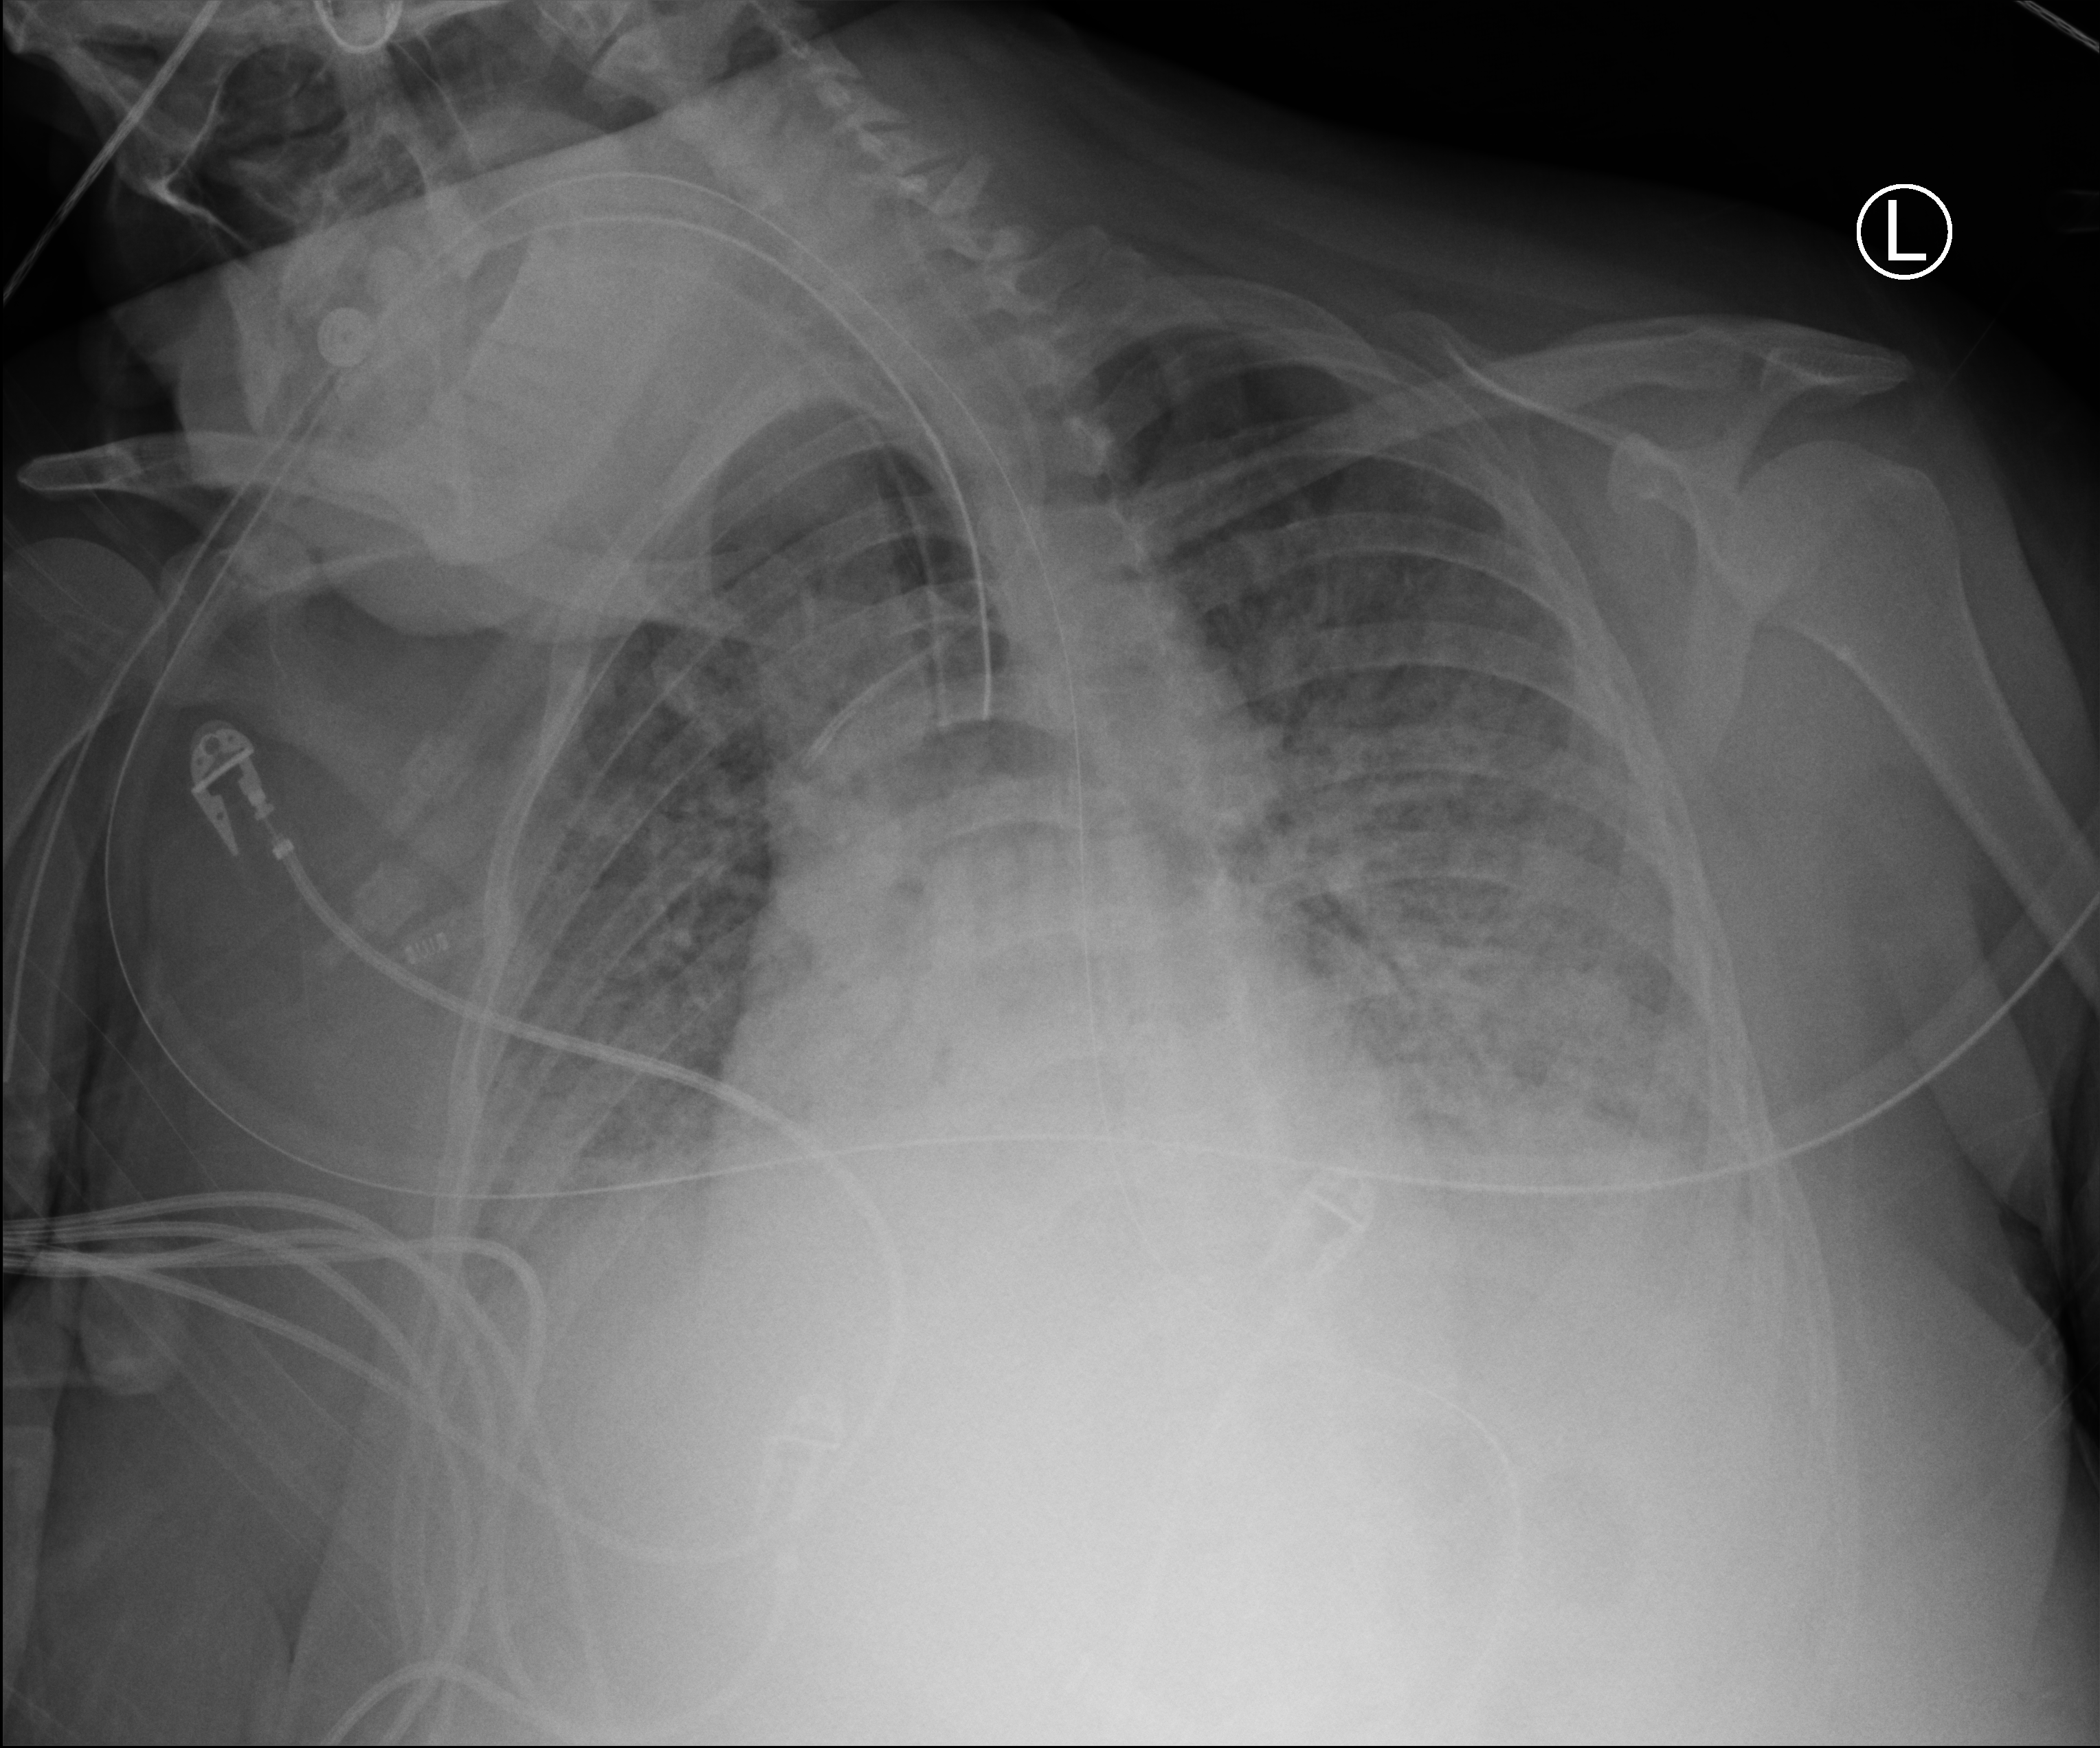
Portable chest radiograph, anteroposterior (AP) projection. Female patient hospitalised with COVID-19, age 18–59 years.
From the hospital-stay record, not from the radiograph (when in the stay this image was taken is not recorded): mechanically ventilated during this hospital stay: yes; admitted to intensive care during this hospital stay: no.